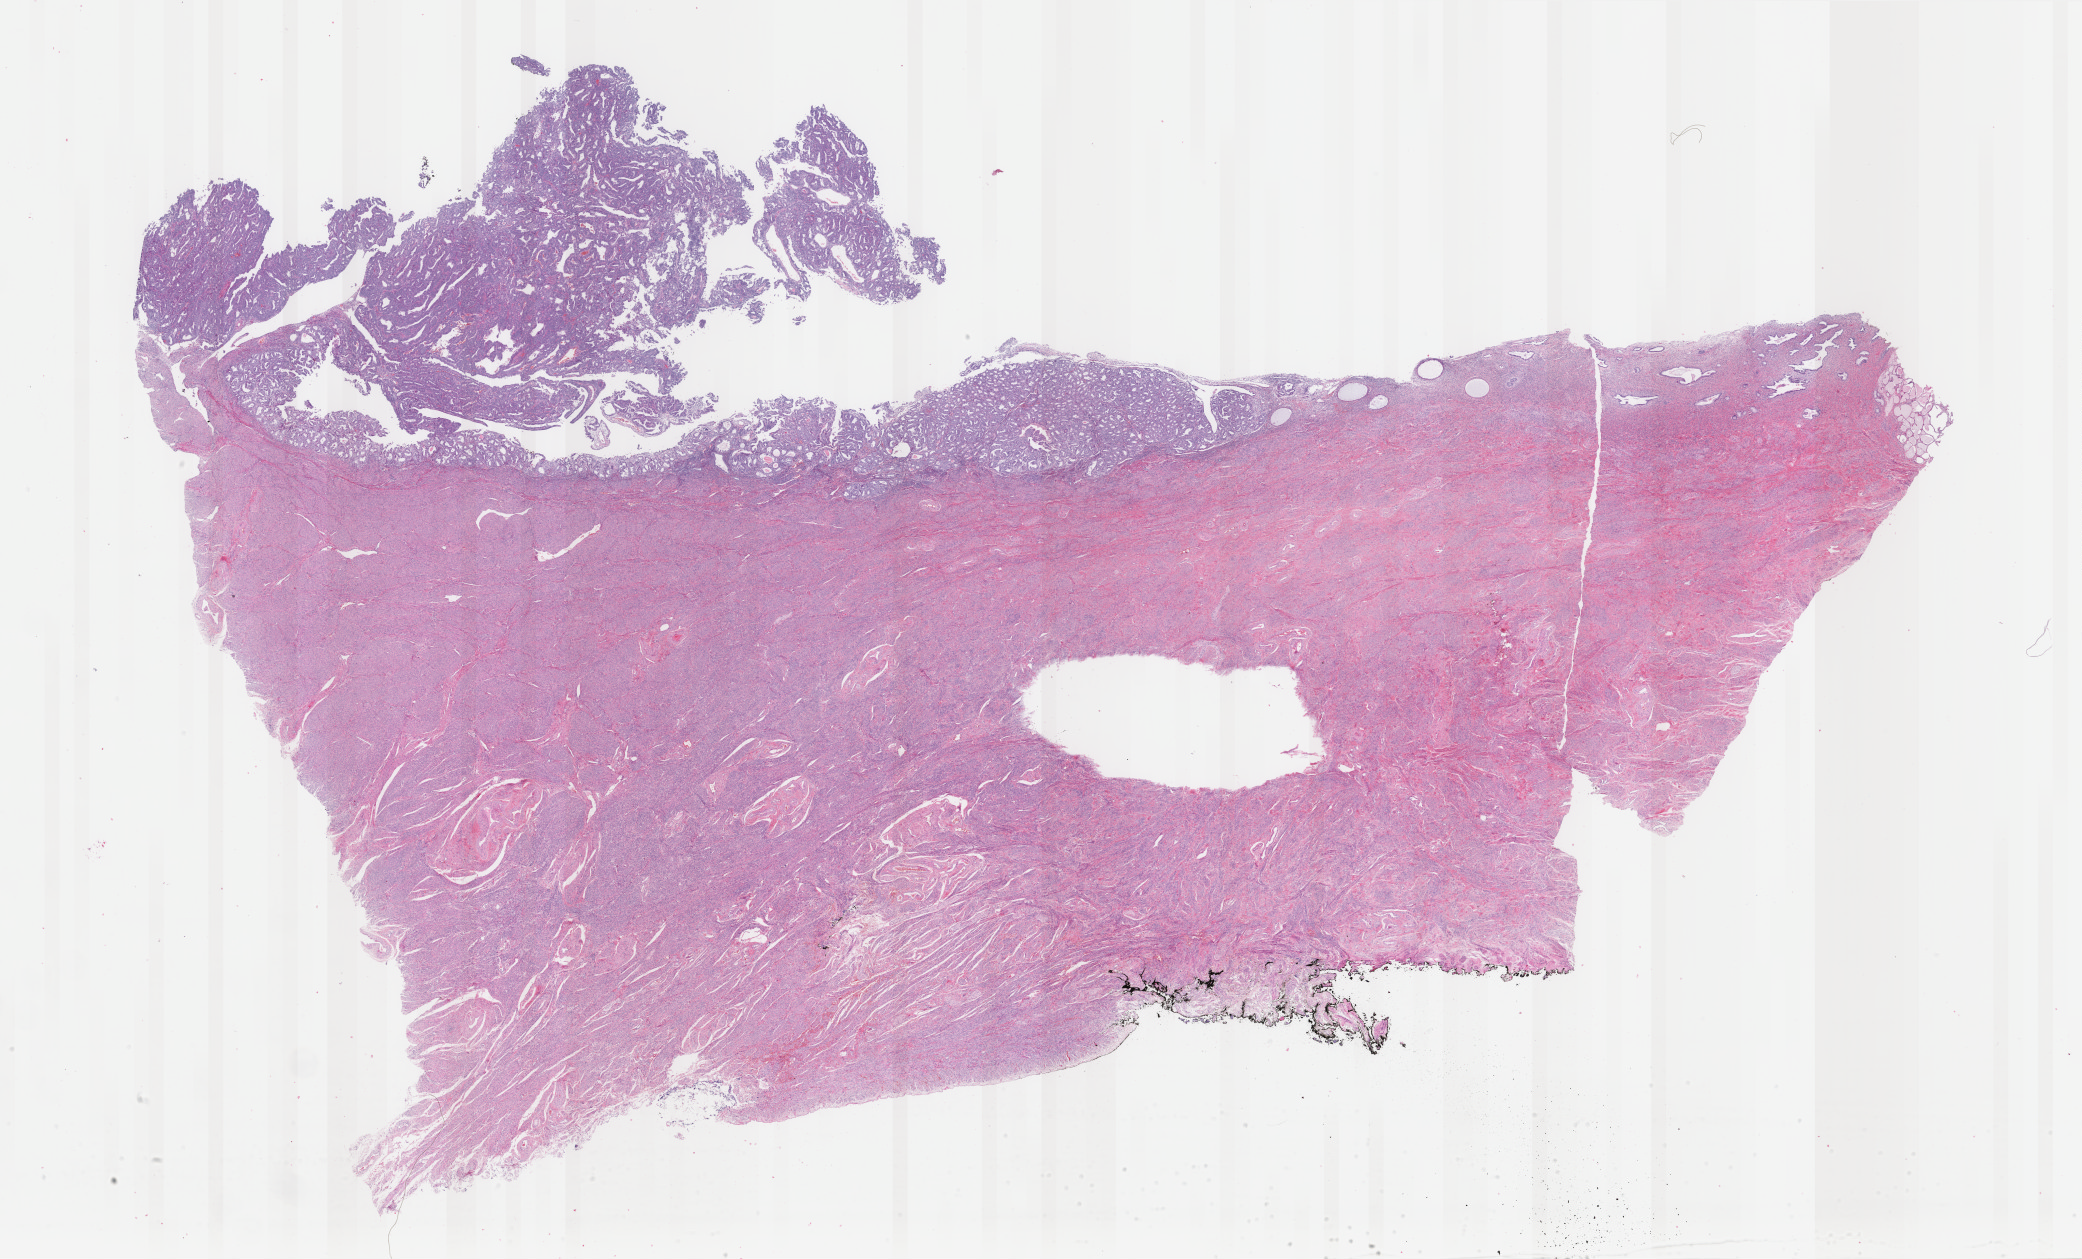
Hematoxylin and eosin (H&E) stained whole-slide image — a low-resolution overview of the entire scanned area, about 33.1 x 20.0 mm. FFPE section. Uterus, primary tumour sample. Female patient; age at initial diagnosis 55 years. Histologic grade: G2 (moderately differentiated).
FIGO stage: IA. Diagnosis: Endometrioid adenocarcinoma, NOS (endometrium). Lymph nodes positive (case pathology): 0 of 13 examined.